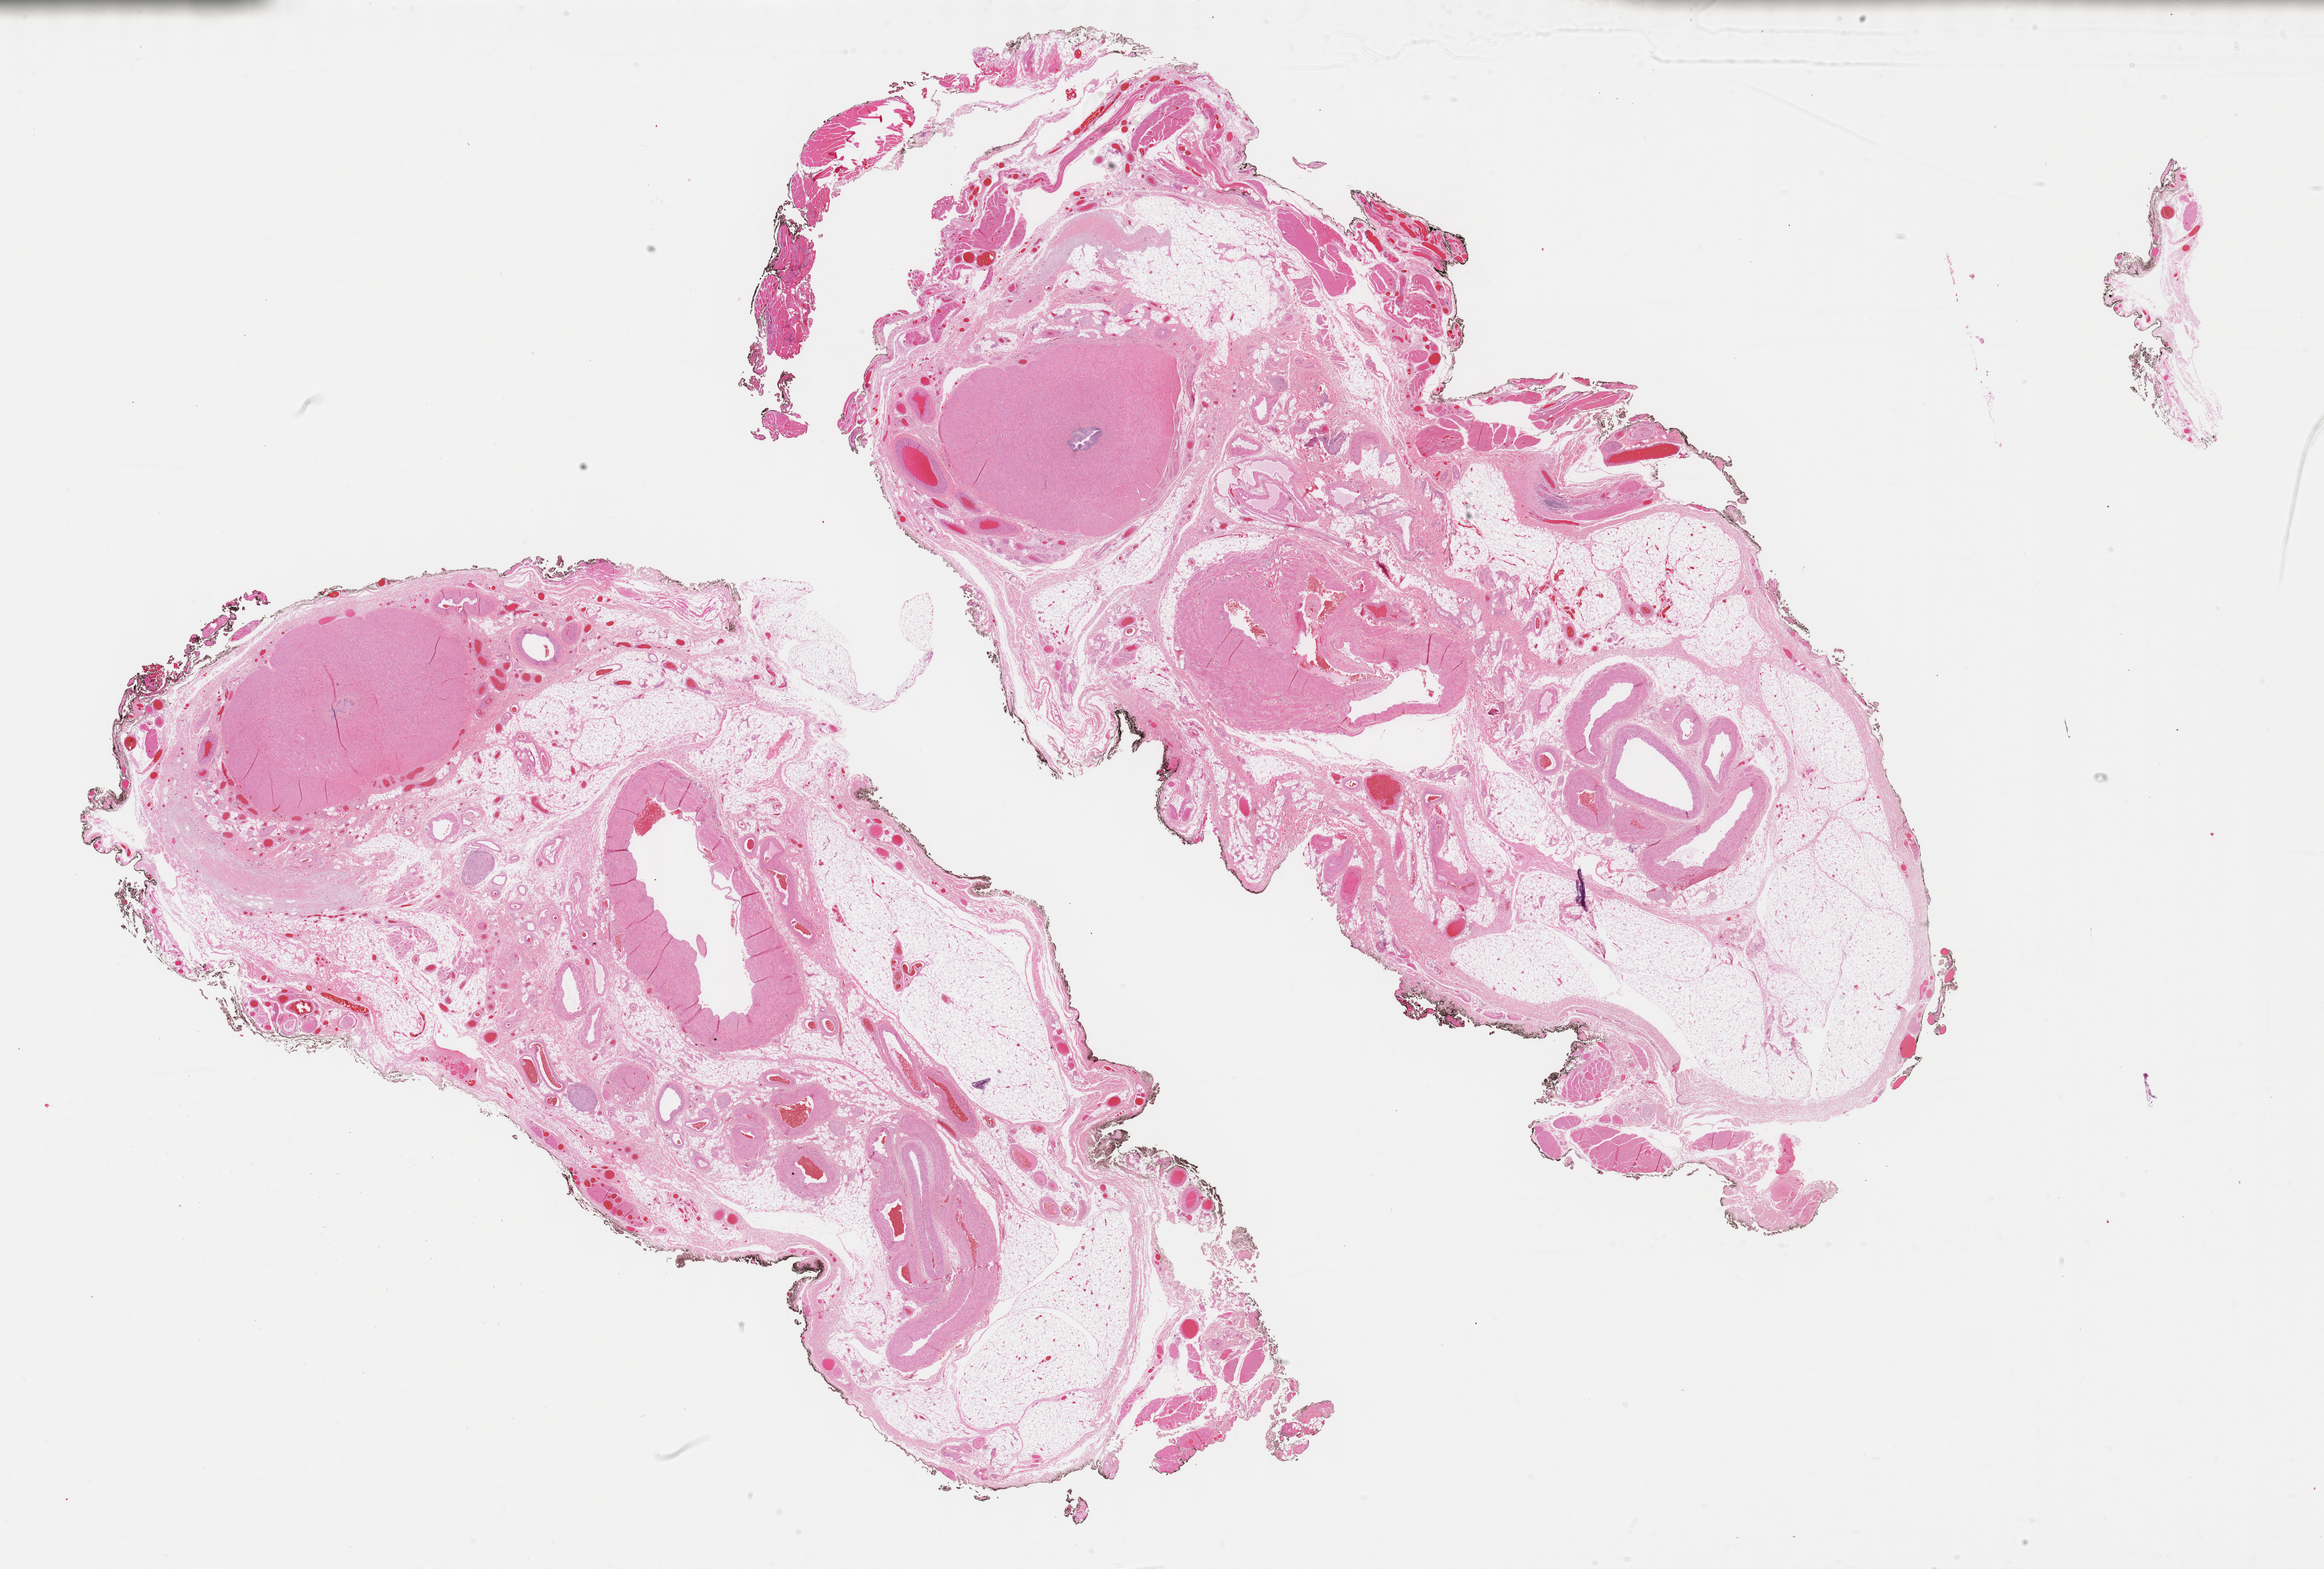
Digitized Hematoxylin and eosin (H&E) stained tissue section (whole slide), a low-resolution overview of the entire scanned area, about 32.7 x 22.1 mm (from a 40x scan); FFPE section; sample: primary tumour, testis. Patient: male, age at initial diagnosis 38 years.
- laterality: left
- histologic diagnosis: Seminoma, NOS